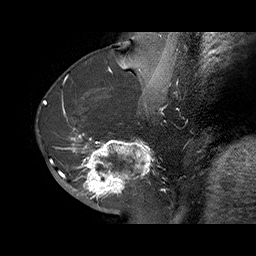
Breast MRI (dynamic contrast-enhanced), one sagittal slice; position 29 of 70 along the scan axis; dynamic contrast-enhanced series, time point 2 of 6 at this slice position (early post-contrast); 1.5 T; TE 4.5 ms, TR 32.4 ms; 3 mm slice thickness; 256 × 256 image matrix, field of view 180 × 180 mm. Female patient. From the clinical record (not read from this slice): setting: breast cancer imaged before/during neoadjuvant chemotherapy; receptor status: HR-positive, HER2-negative.
Outlined on this slice (semi-automatic segmentation, software-assisted and operator-edited):
- analysis volume of interest (the breast-tissue region the enhancement analysis was run in; not a lesion): bounding box [x1, y1, x2, y2] px = [71, 128, 159, 202]
- tumour enhancement mask (voxels above the 100 % enhancement threshold inside the analysis volume of interest): [71, 128, 152, 200]